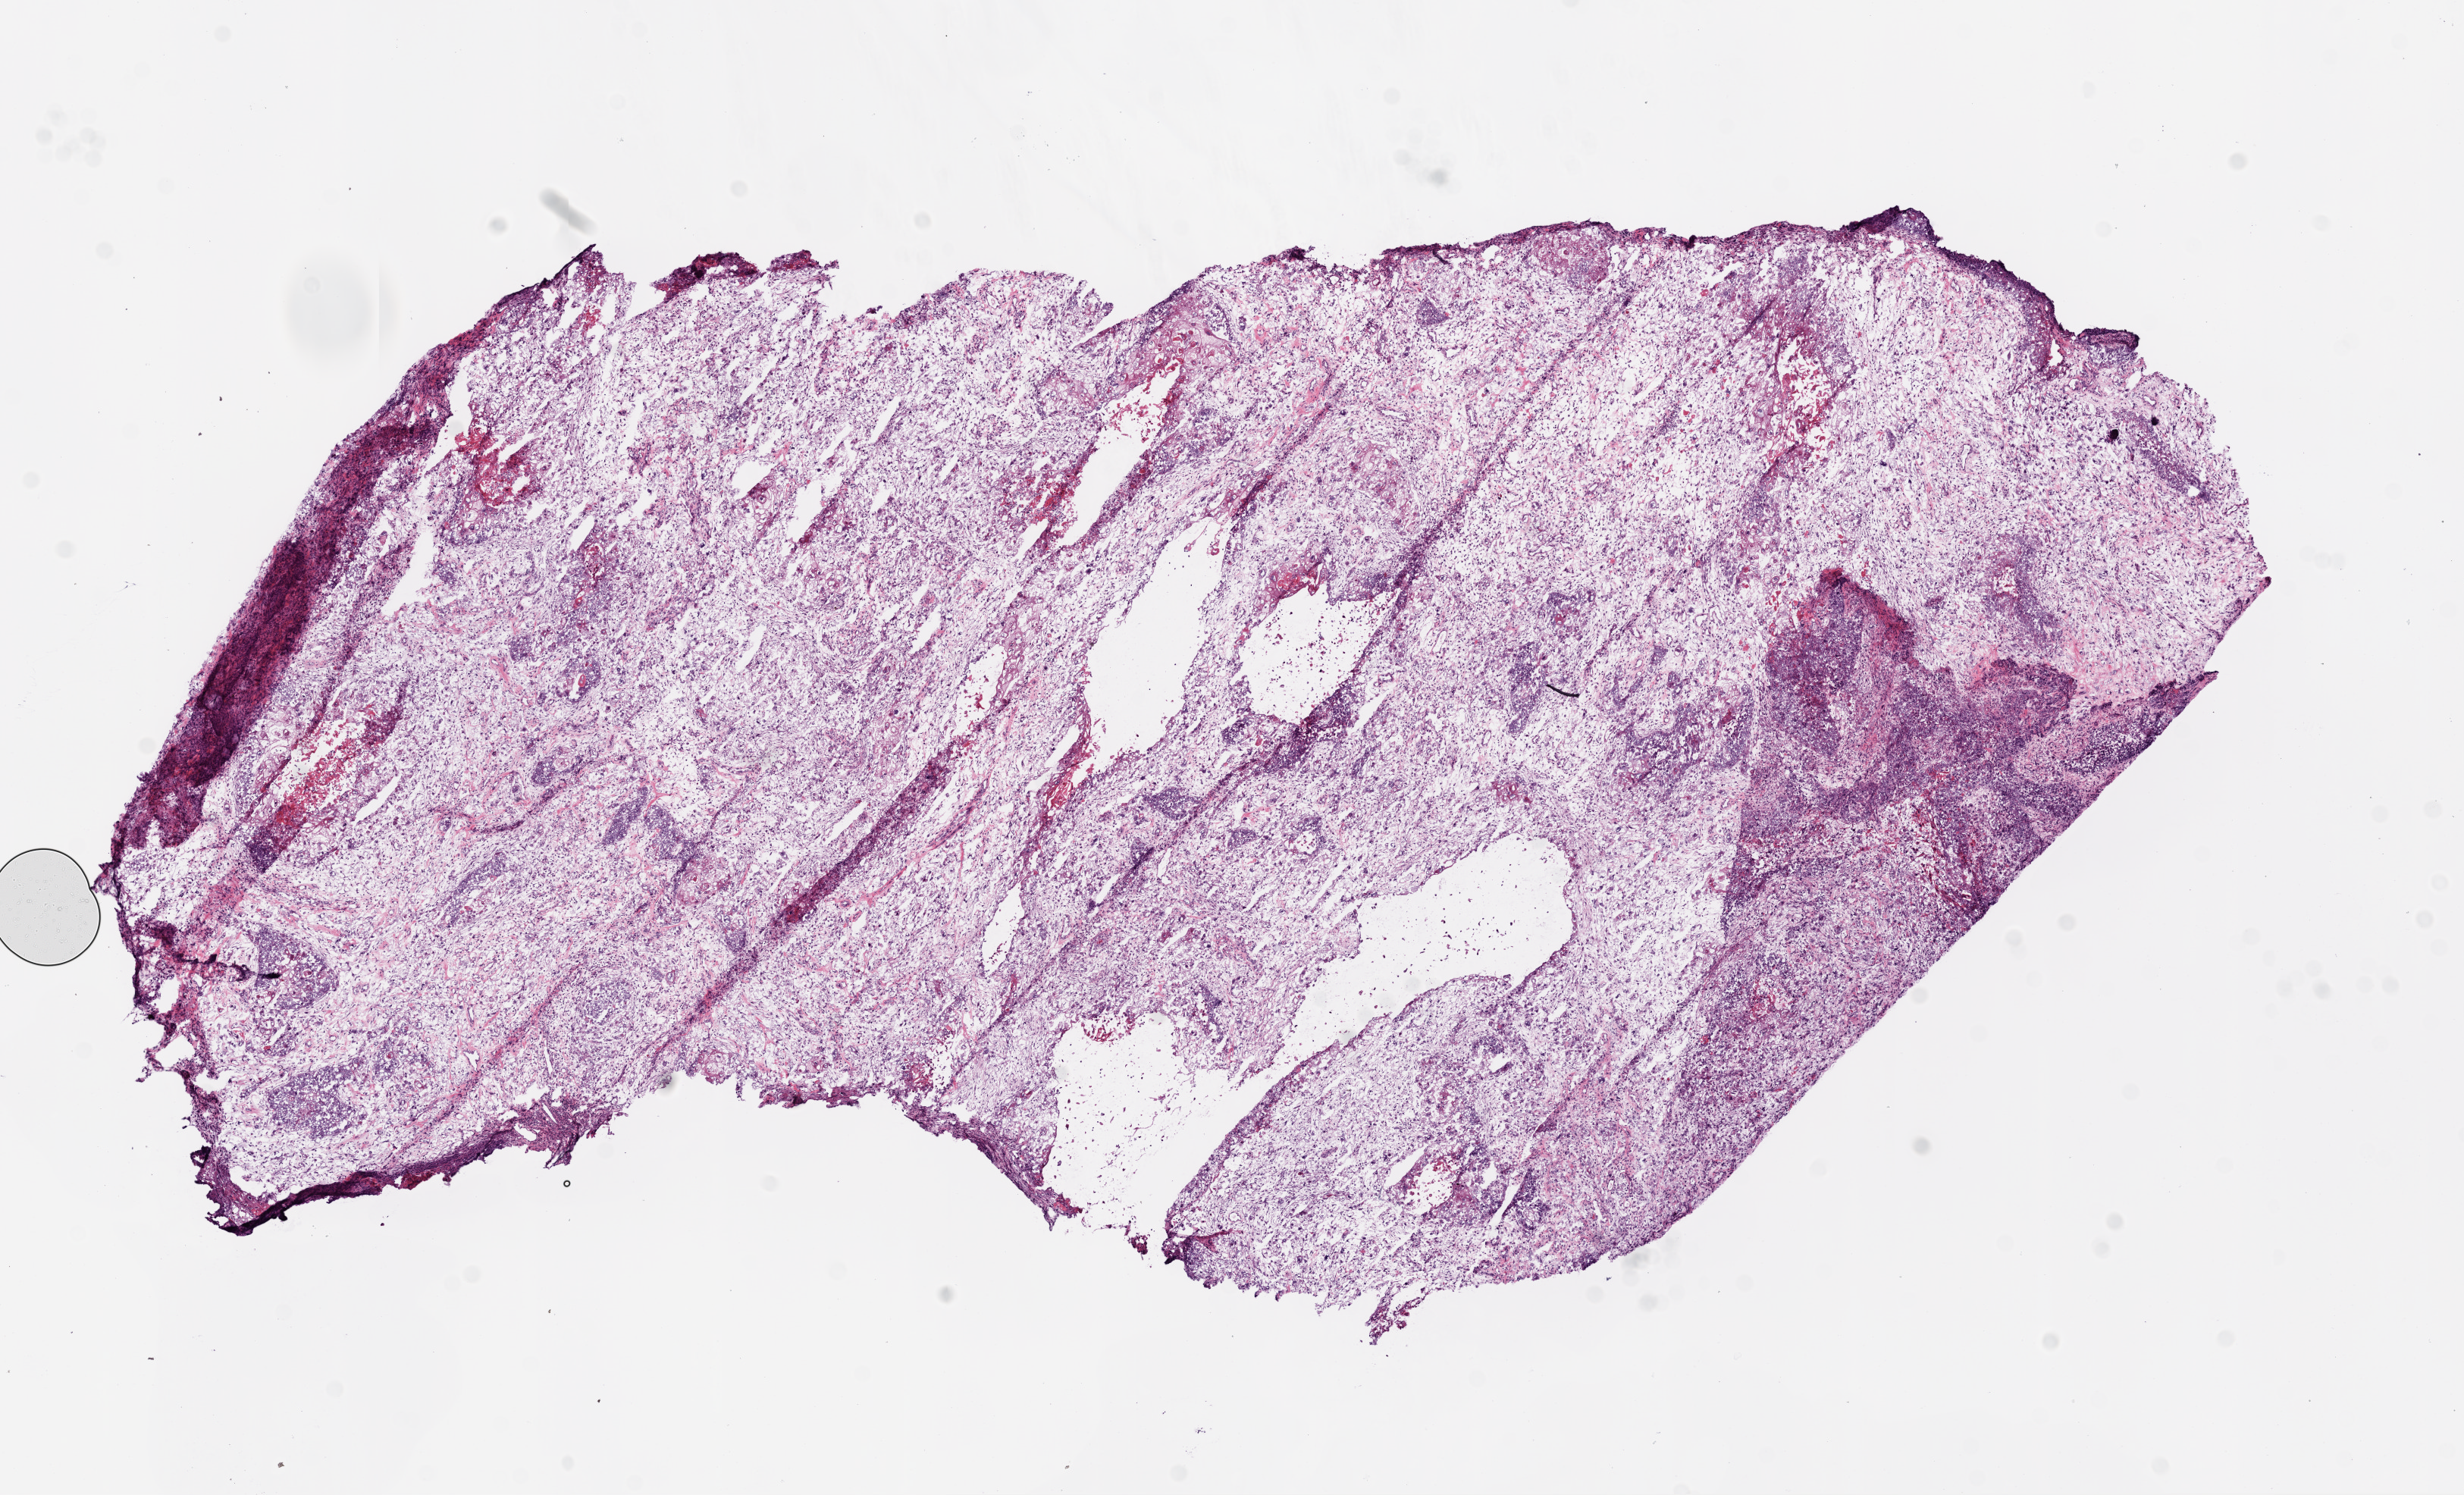
Digitized H&E tissue section (whole slide), low-resolution overview of the scanned area, about 13.0 x 7.9 mm, frozen section from the bottom of the tissue portion, primary tumour sample from the lung. Female, age 64 years at initial diagnosis. Composition of this section per pathologist review: tumour cells 70%, tumour nuclei 70%, normal cells 0%, stromal cells 20%, necrosis 10%.
• TNM: T2 N1 M0
• laterality: left
• AJCC pathologic stage: IIB
• pathologic diagnosis: Squamous cell carcinoma, NOS (lower lobe, lung)